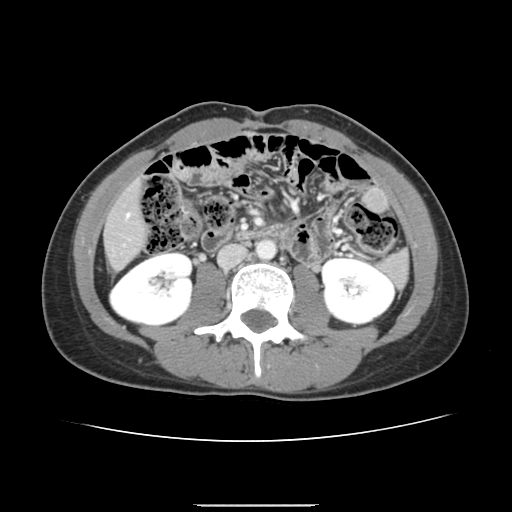
Contrast-enhanced abdominal CT, one axial slice. Slice 43 of 150 in the series (ordered by position). Intravenous contrast given. Soft-tissue window (W 400 / L 40 HU). 2.5 mm slice thickness. 512 × 512 image matrix, field of view 324 × 324 mm. Female patient, age 32 years. Case-level facts recorded for this patient, not image findings: diagnosis: colorectal cancer liver metastases, imaged before liver resection; multiple liver metastases: yes; largest metastasis: 0.7 cm; disease in both lobes: no.
Structures marked on this image (outlined manually by an expert reader):
- hepatic veins: bounding box (x1, y1, x2, y2) in pixels: (127, 214, 130, 216)
- liver: (106, 186, 146, 269)
- planned liver remnant (the part of the liver to remain after resection): (106, 186, 146, 269)